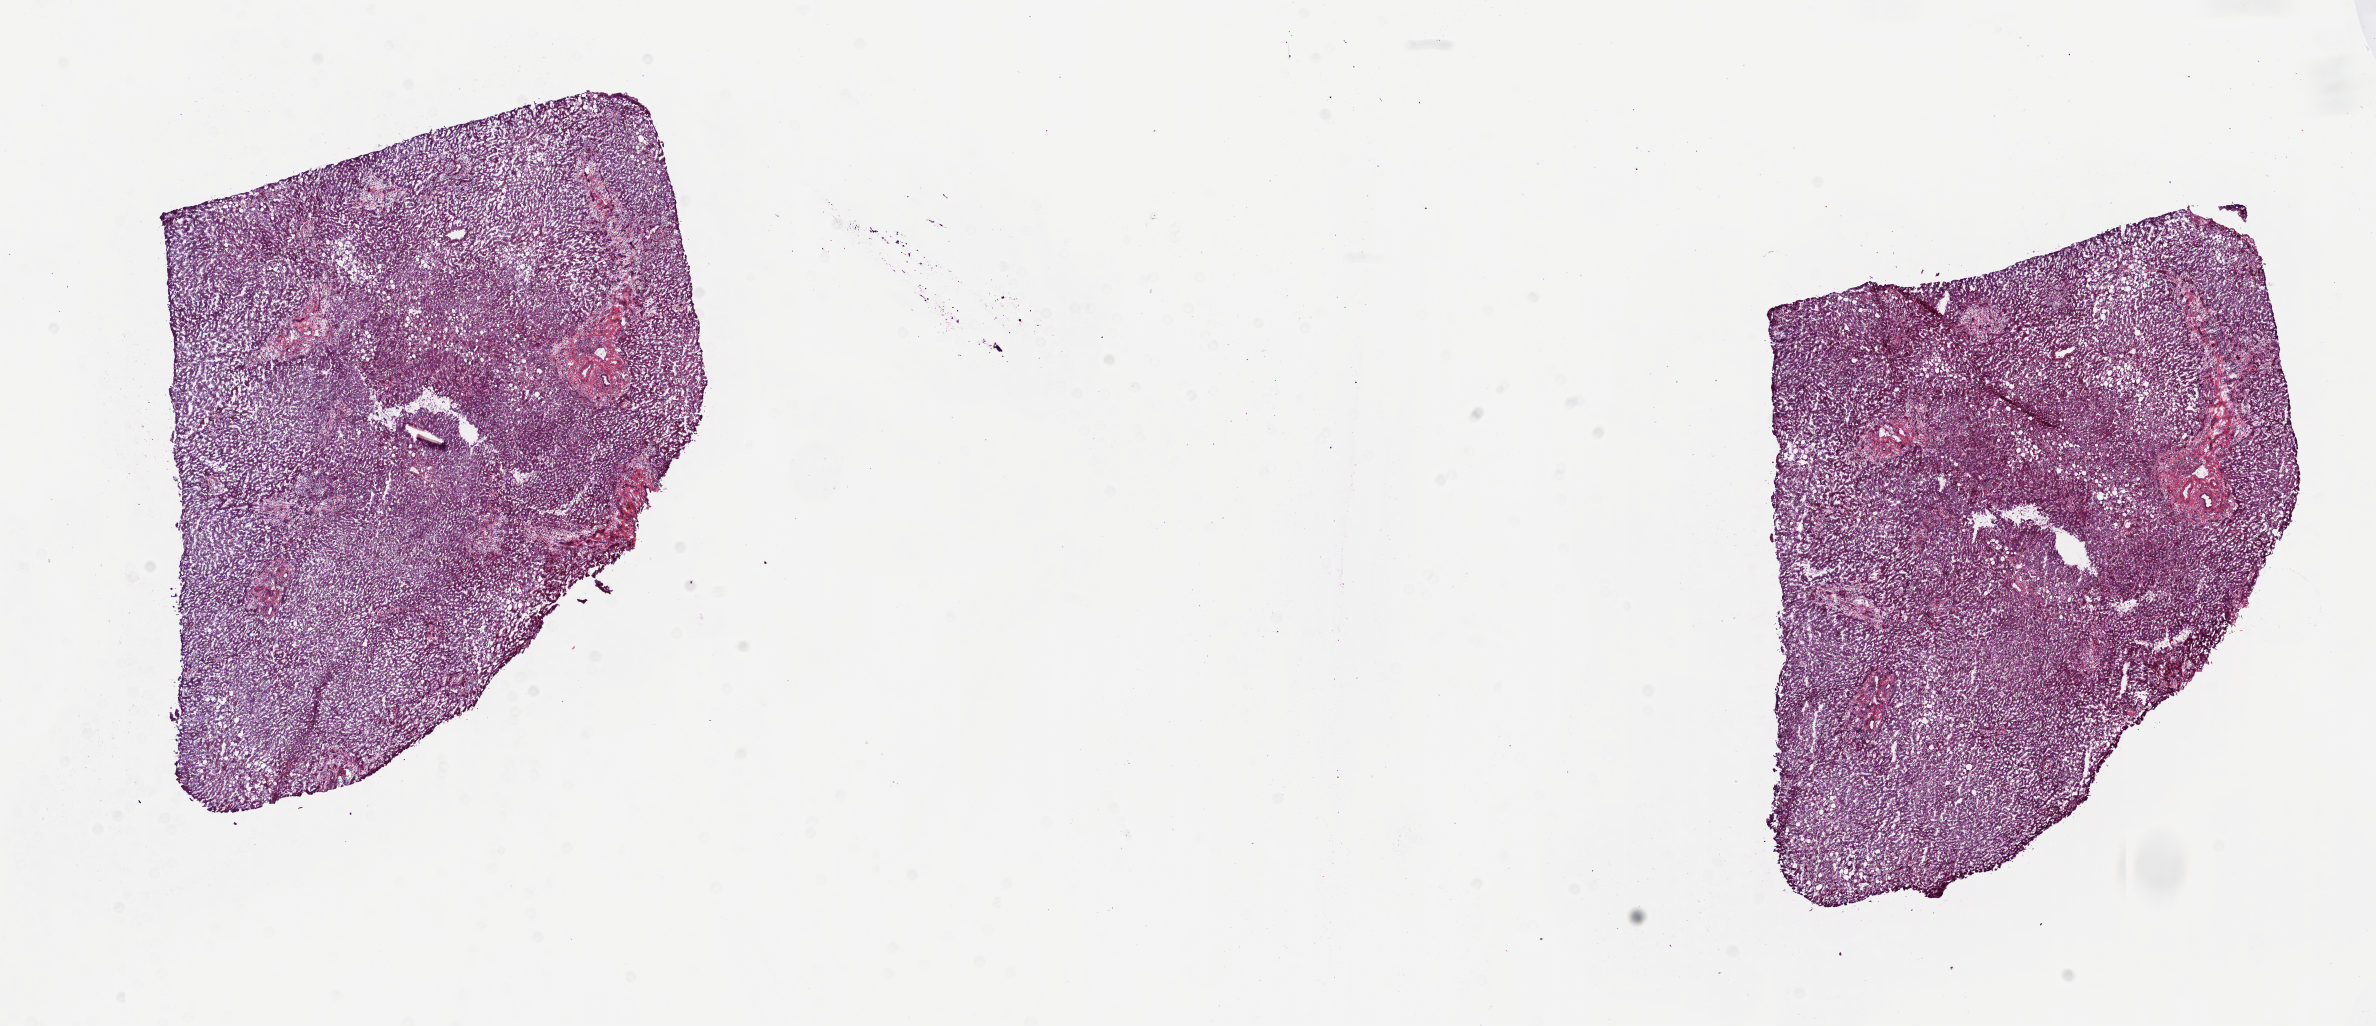
Digitized Hematoxylin and eosin (H&E) stained tissue section (whole slide), whole scanned area (about 18.8 x 8.1 mm, from a 20x scan) shown as a low-resolution overview, frozen section from the top of the tissue portion, bile duct, solid tissue normal (non-tumour tissue) sample. Male, age 67 years at initial diagnosis. Pathologist review of this section (percent, as recorded): tumour cells 0%, tumour nuclei 0%, normal cells 94%, stromal cells 6%, necrosis 0%. Inflammatory infiltration, as recorded: lymphocyte infiltration 4%, monocyte infiltration 1%, neutrophil infiltration 0%.
- this section: solid tissue normal sample (biorepository sample class)
- patient diagnosis: Cholangiocarcinoma